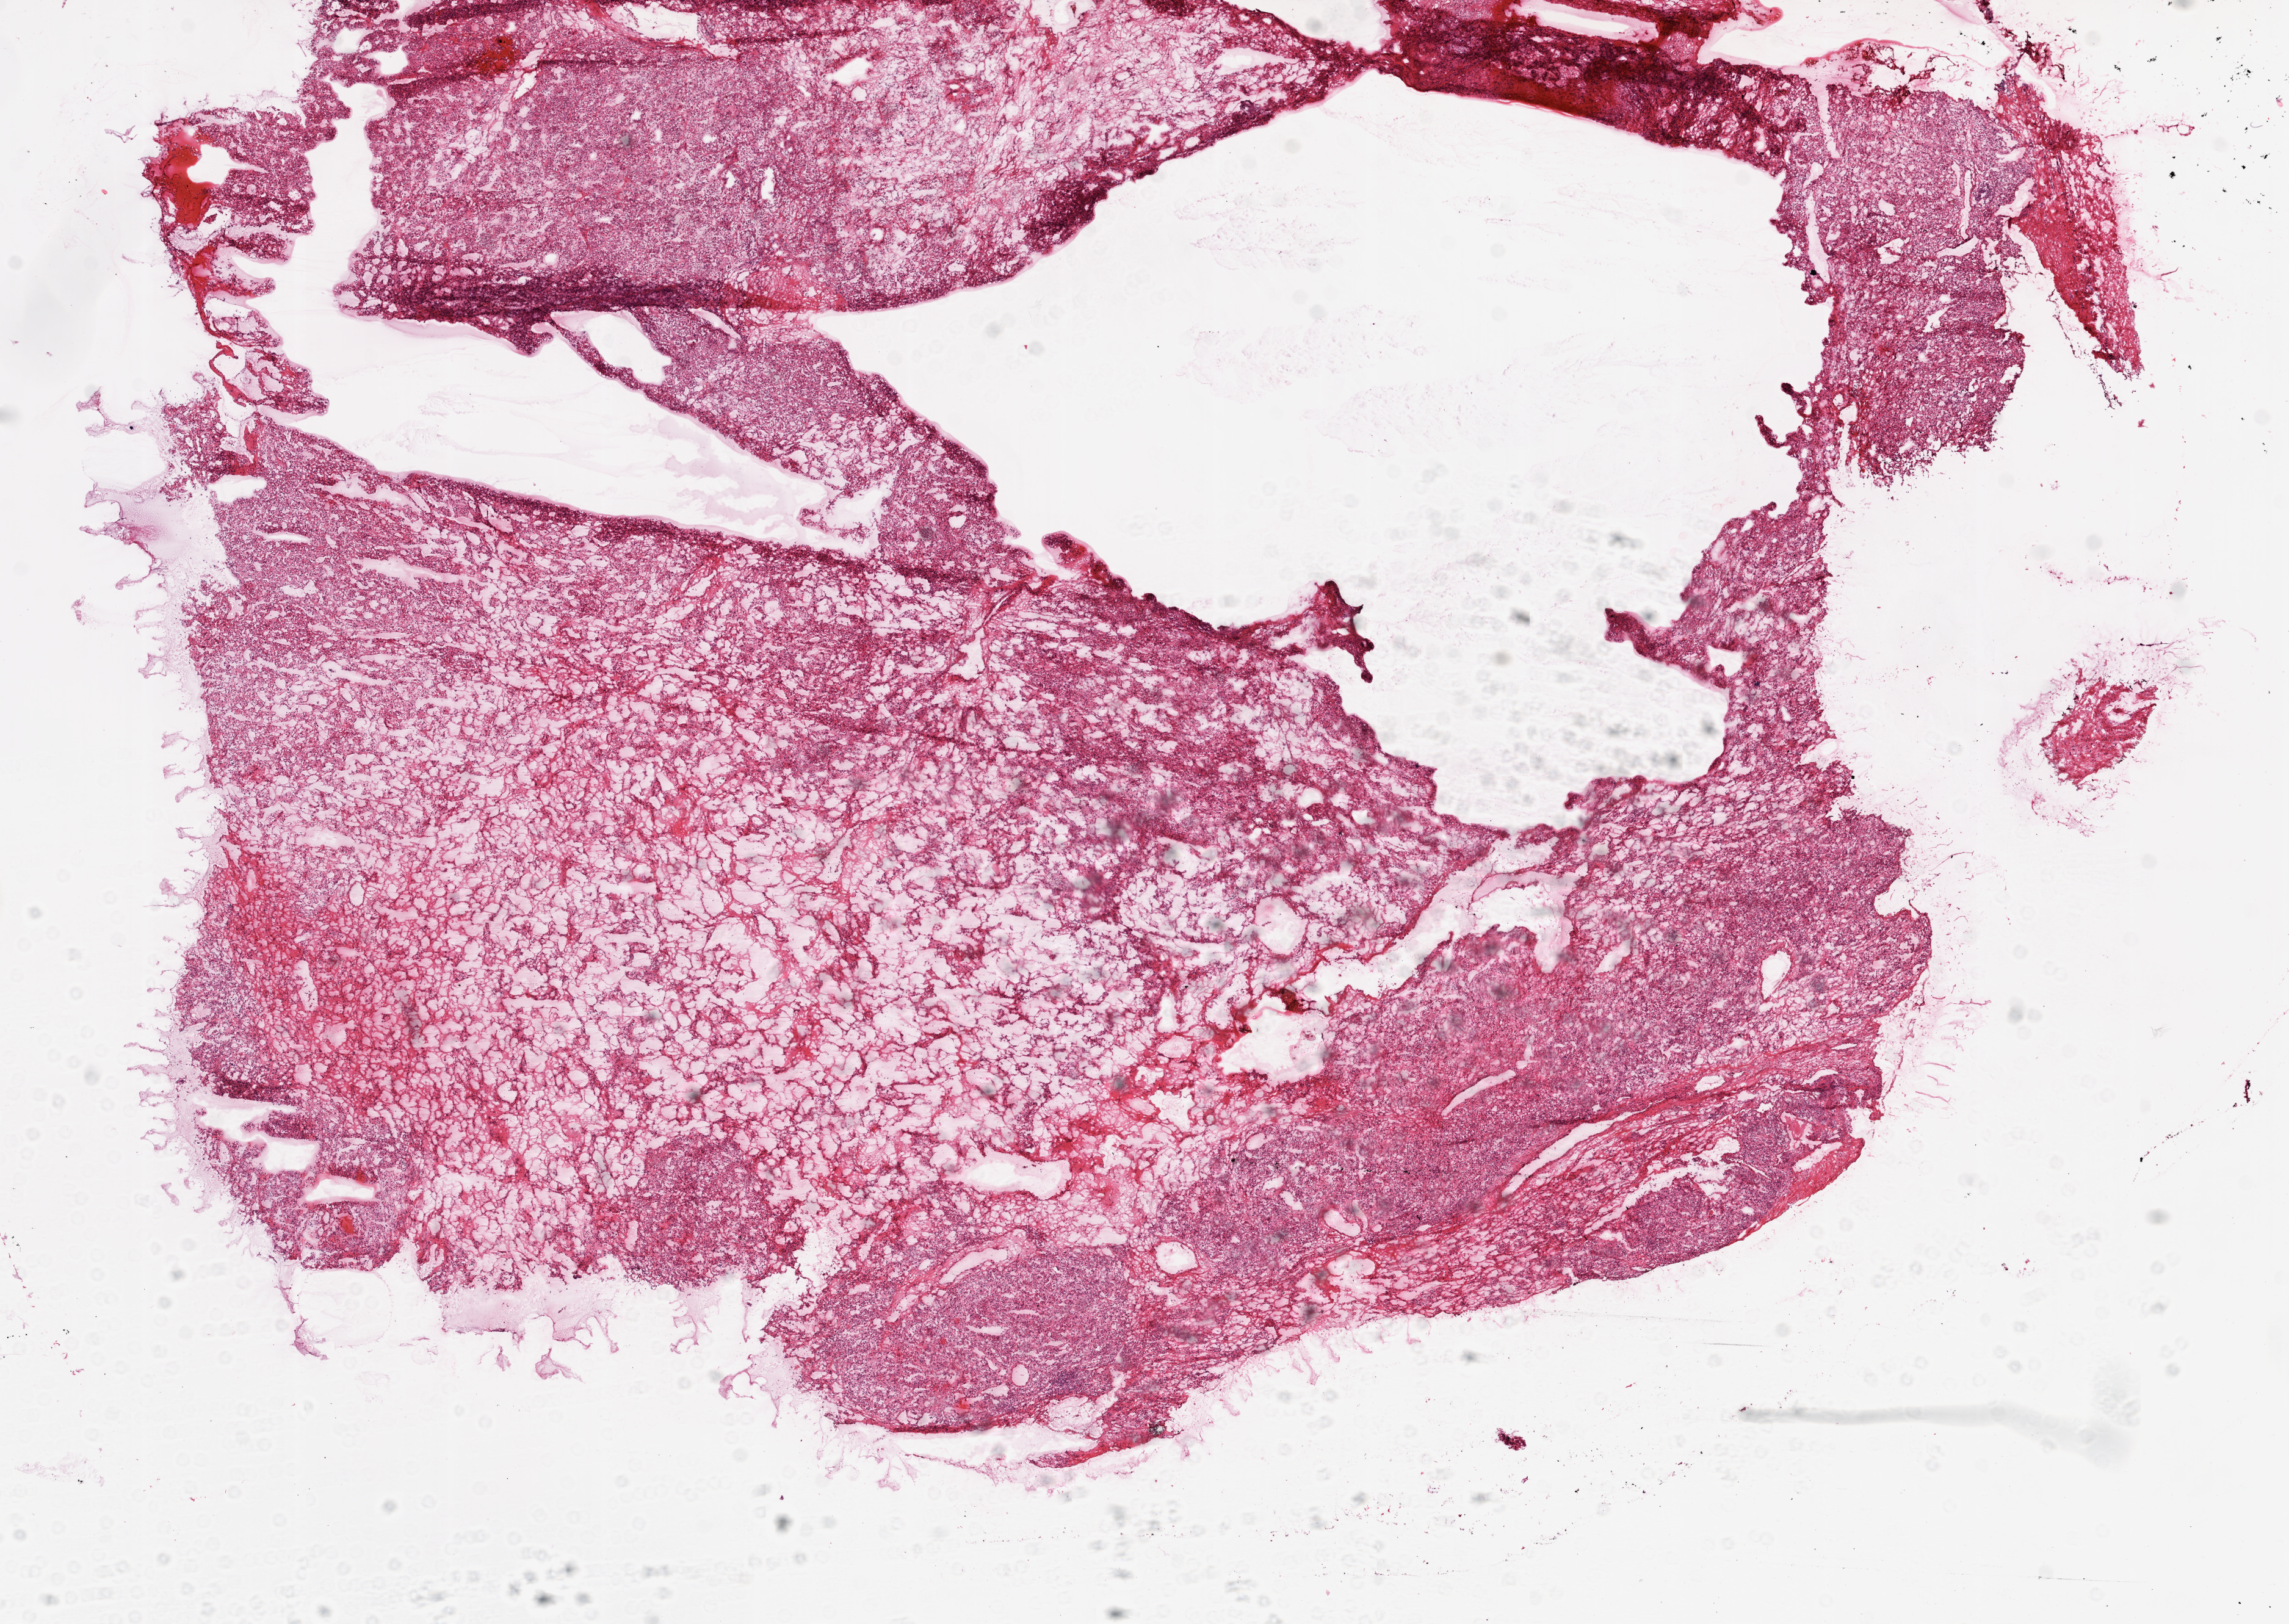
Whole-slide histology image, Hematoxylin and eosin (H&E) stained — whole scanned area (about 15.0 x 10.7 mm, slide scanned at 20x) shown as a low-resolution overview. Frozen section from the top of the tissue portion. Kidney, primary tumour sample. Patient: female, age at initial diagnosis 71 years. Histologic grade: G2 (moderately differentiated). Pathologist review of this section (percent, as recorded): tumour cells 80%, tumour nuclei 80%, normal cells 0%, stromal cells 20%, necrosis 0%.
AJCC pathologic stage: I (6th edition). Diagnosis: Clear cell adenocarcinoma, NOS.